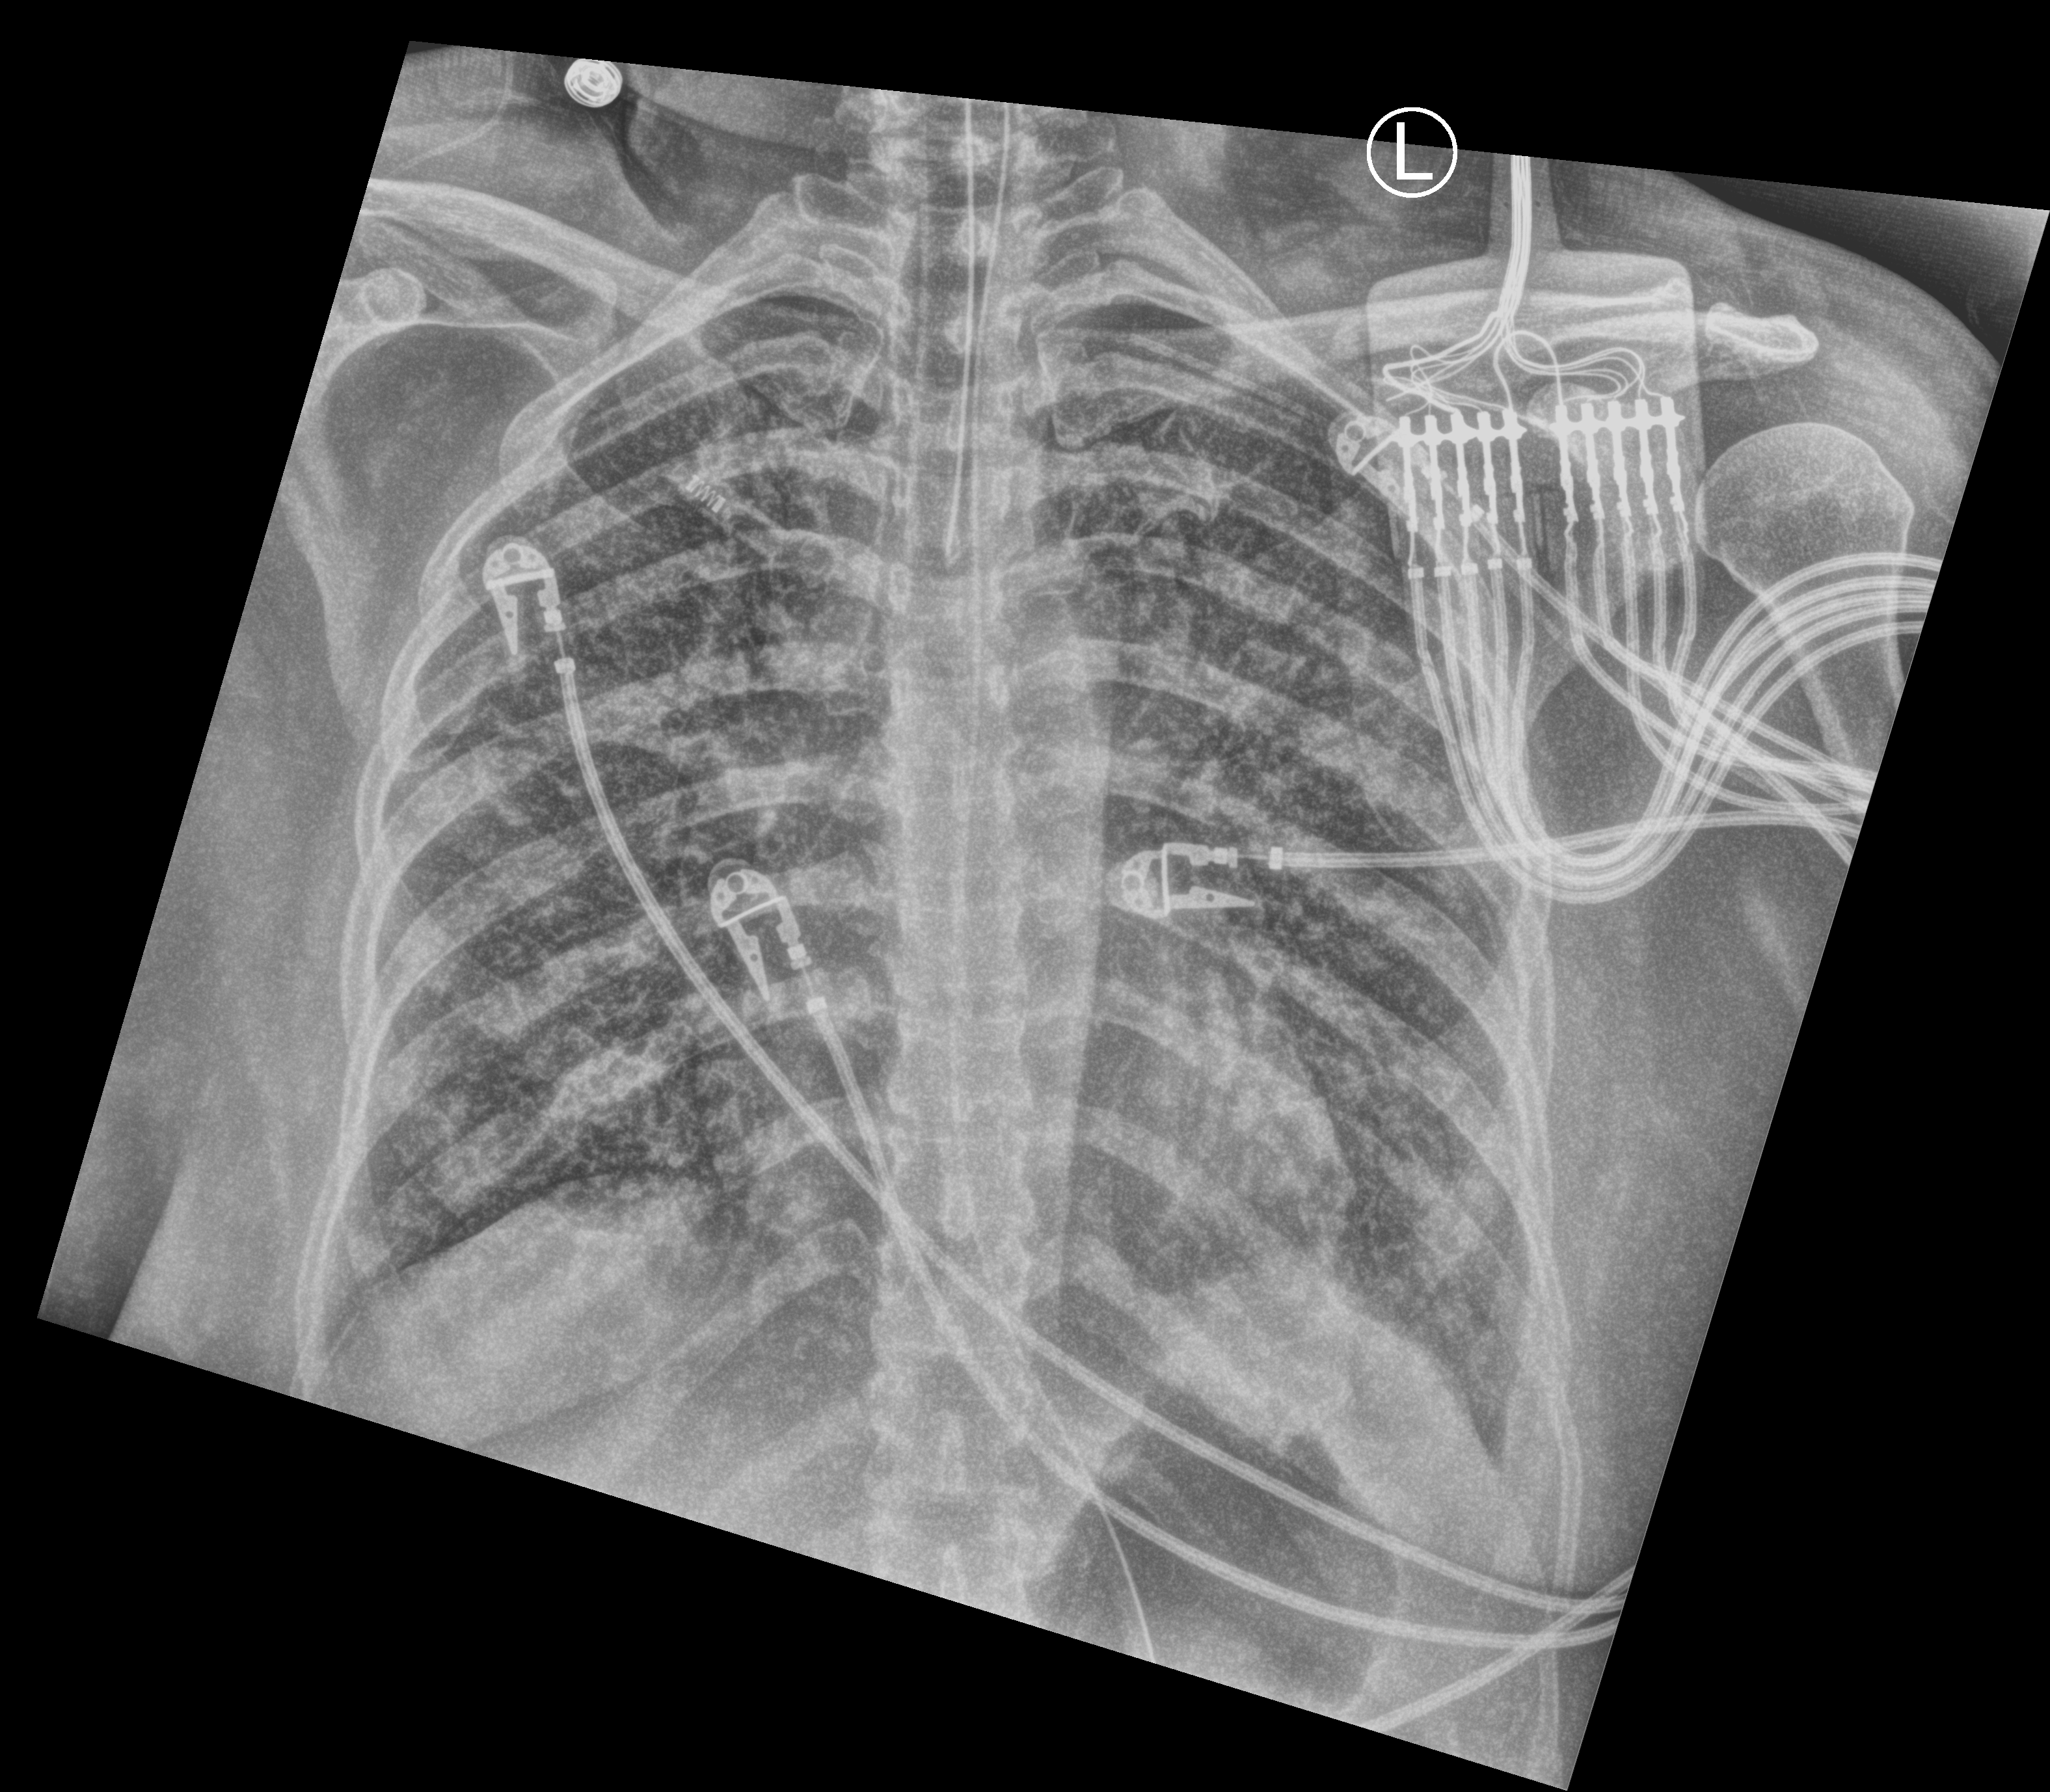
Bedside chest radiograph (computed radiography); anteroposterior (AP) projection. Male patient hospitalised with COVID-19, age 18–59 years.
From the hospital-stay record, not from the radiograph (when in the stay this image was taken is not recorded): admitted to intensive care during this hospital stay: yes; length of hospital stay: 38 days.